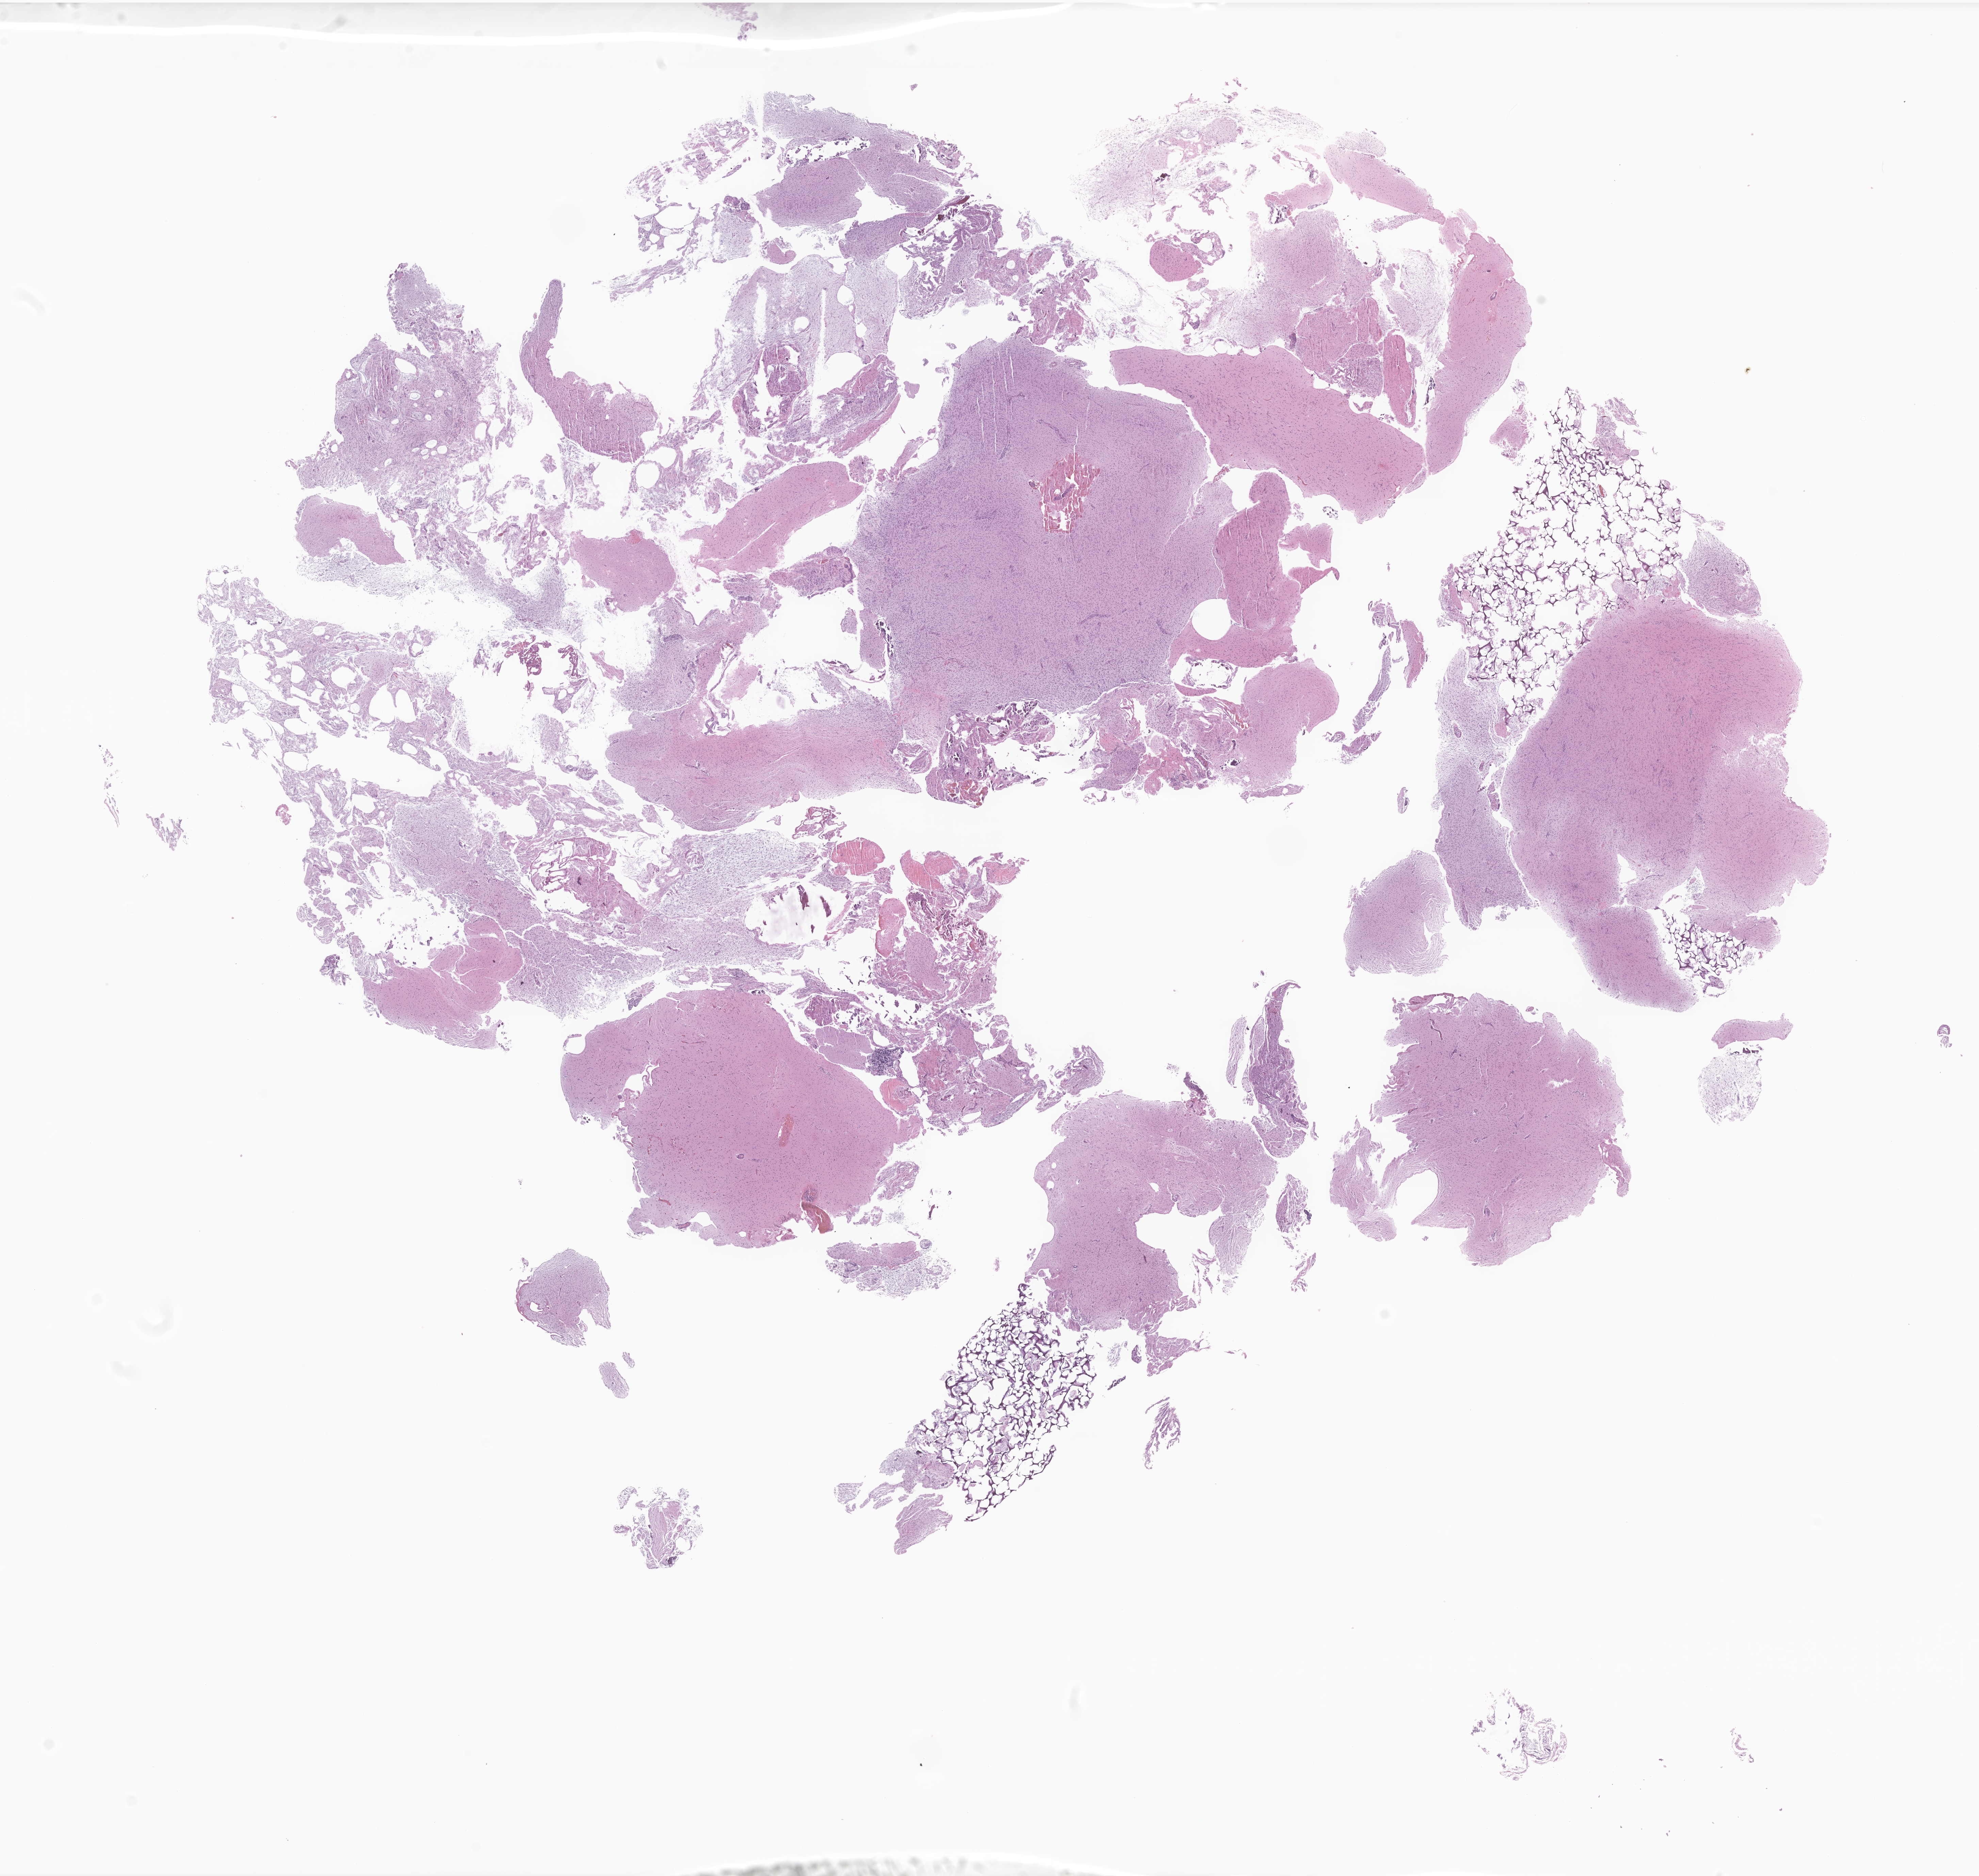
Whole-slide image, hematoxylin and eosin (H&E) stain of tumor tissue from the brain, shown as a low-resolution overview of the whole scanned area (about 24.5 x 23.2 mm), FFPE section. Patient: female, age 37 months (3 years 1 month).
* diagnosis: Neoplasm, uncertain whether benign or malignant